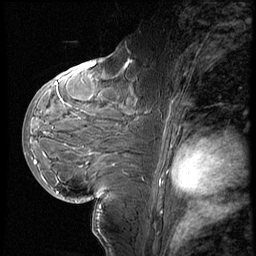
Breast MRI (dynamic contrast-enhanced), one sagittal slice. Position 32 of 60 along the scan axis. 3 images stored at this slice position (order not interpretable as contrast timing). 1.5 T. TE 4.2 ms, TR 8.9 ms. 2.5 mm slice thickness. 256 × 256 image matrix, field of view 200 × 200 mm. Patient: female, 29 years. From the clinical record (not read from this slice): setting: breast cancer imaged before/during neoadjuvant chemotherapy.
Outlined on this slice (semi-automatically segmented with operator editing):
- analysis volume of interest (the breast-tissue region the enhancement analysis was run in; not a lesion): bounding box (x1, y1, x2, y2) in pixels: (29, 57, 152, 200)
- tumour enhancement mask (voxels above the 140 % enhancement threshold inside the analysis volume of interest): (36, 62, 131, 164)